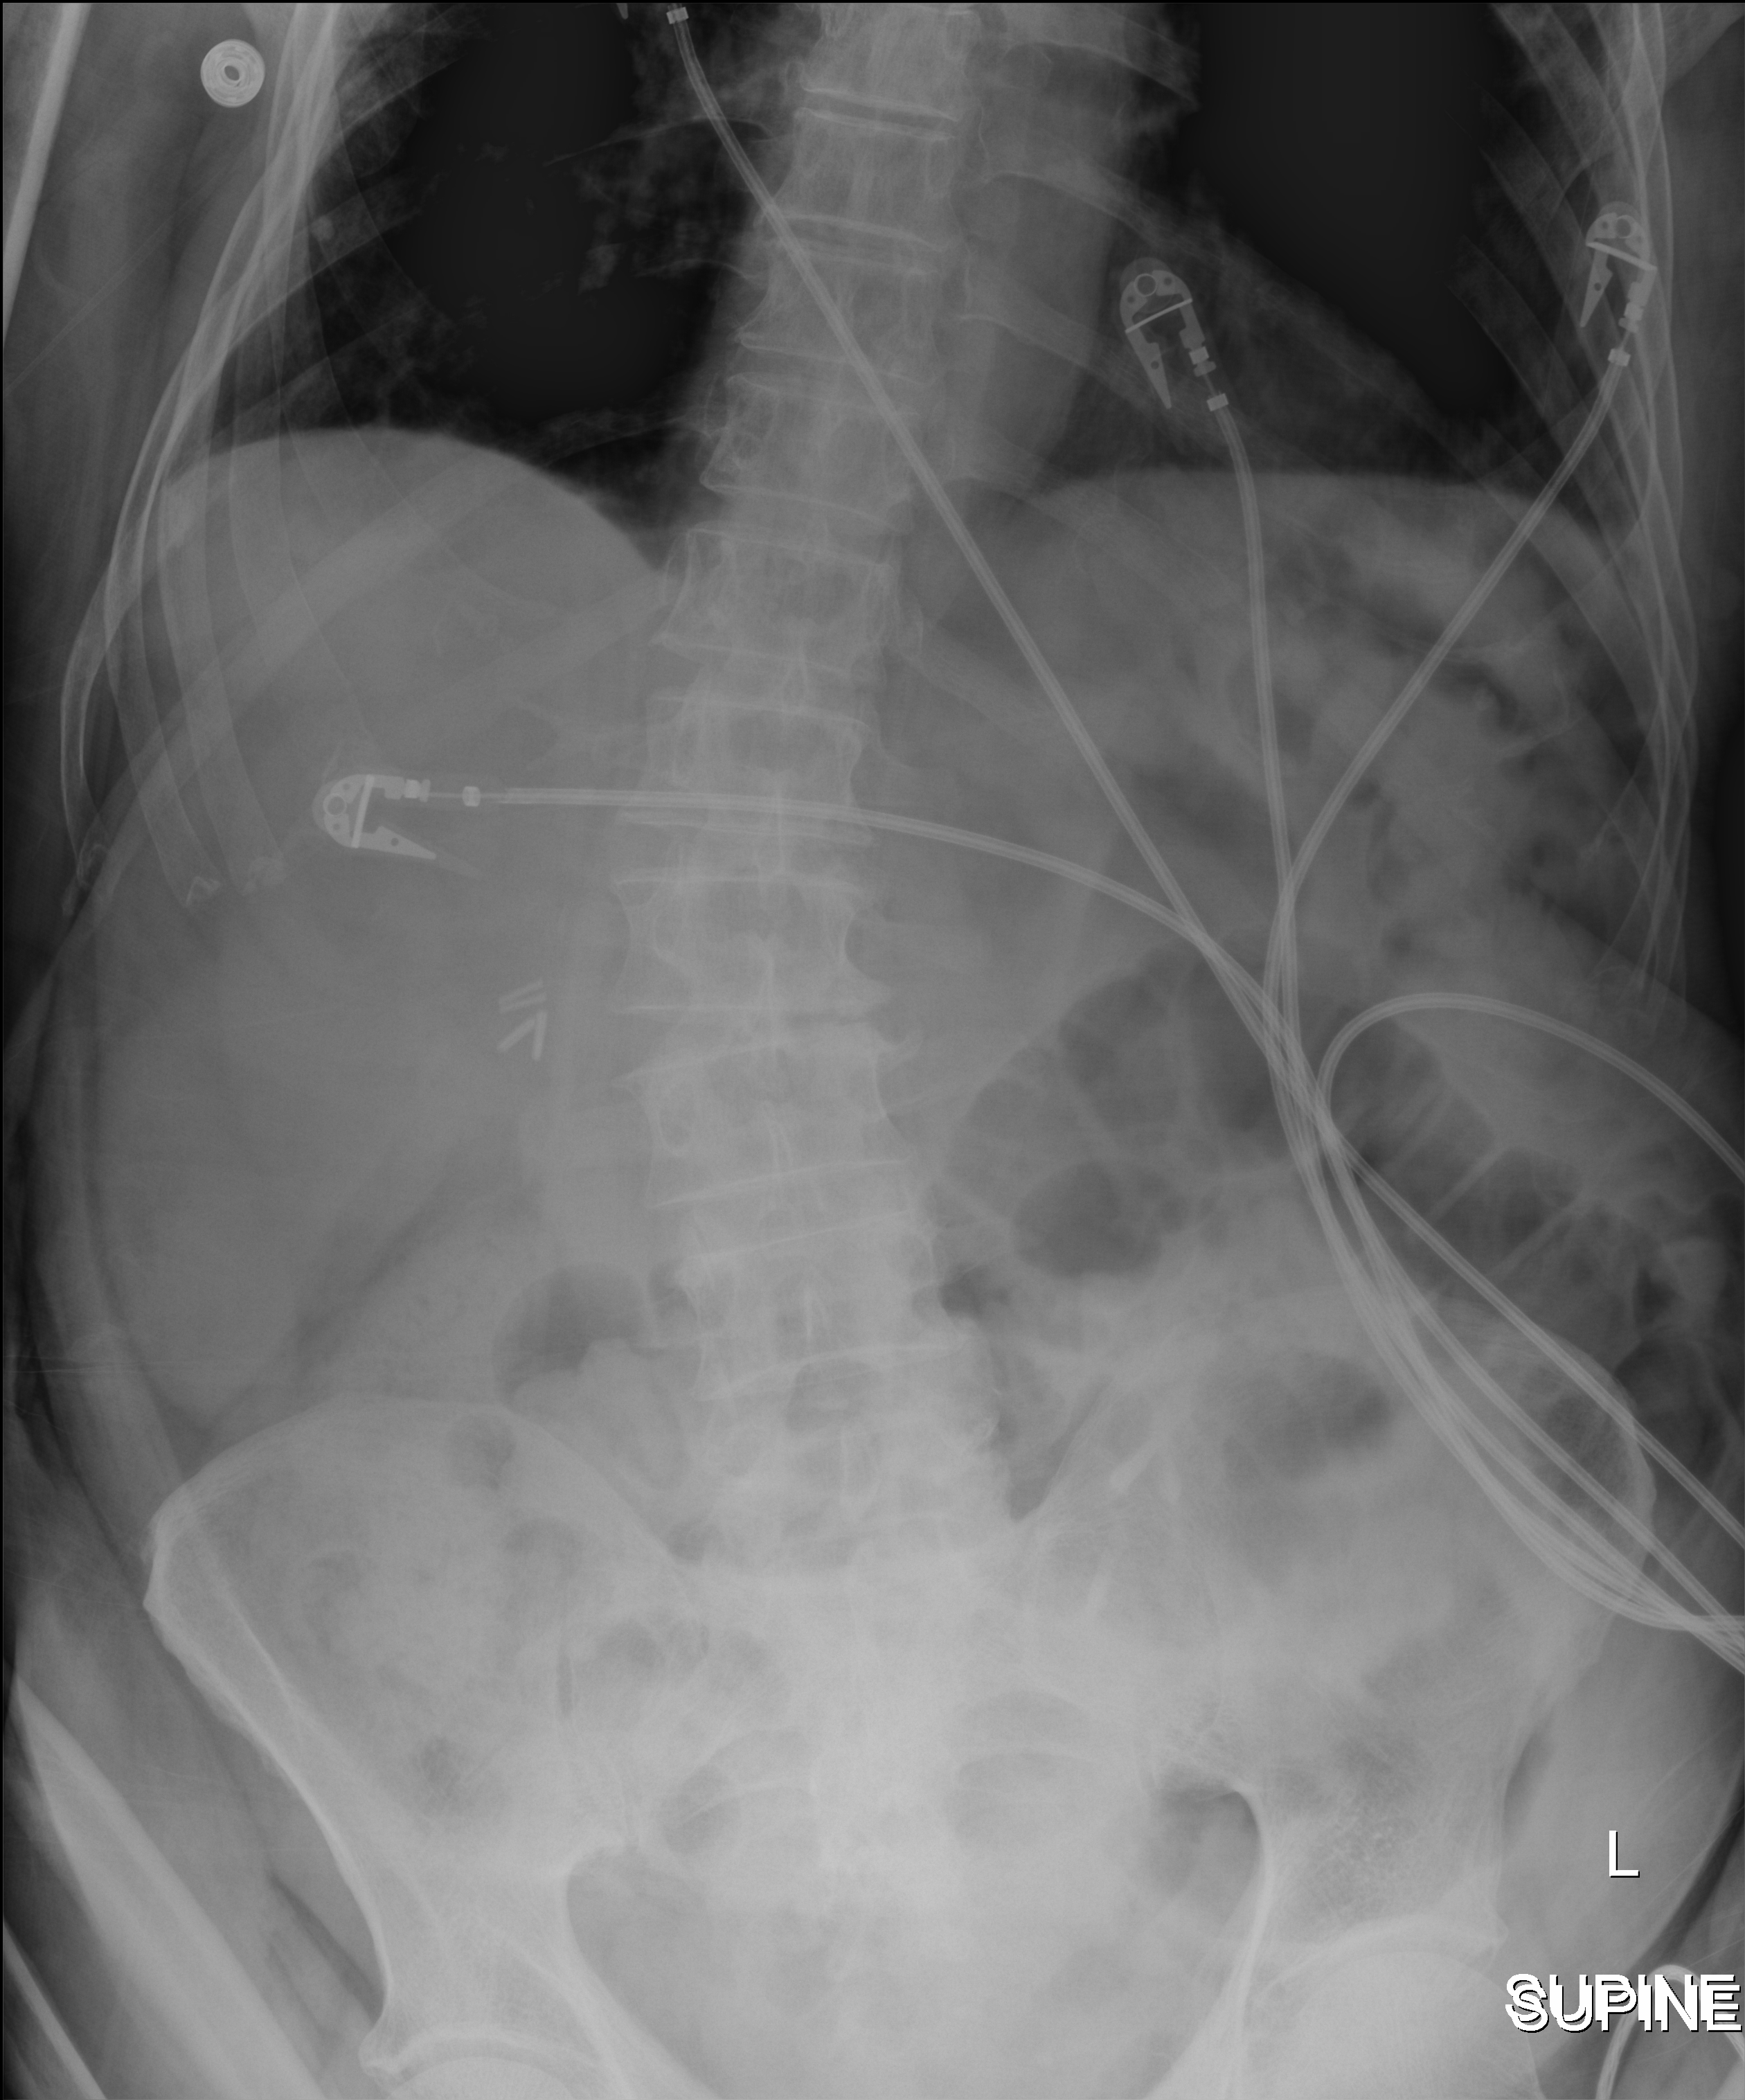
Portable abdomen radiograph, anteroposterior (AP) projection. Male patient hospitalised with COVID-19, age 75–90 years.
Hospital-stay facts (about this admission, not read from this image; timing relative to this image not recorded):
- other chronic lung disease (admission record): yes